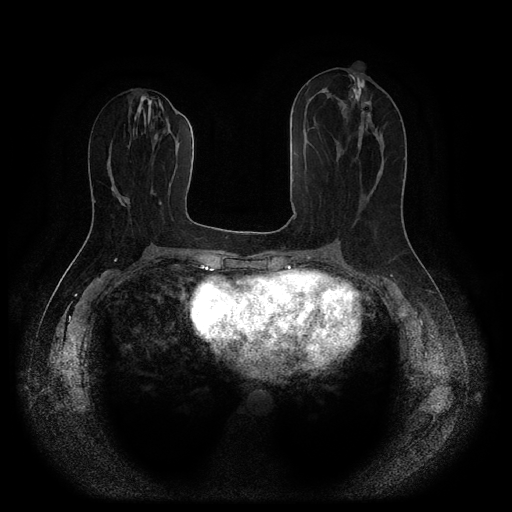
Breast MRI (dynamic contrast-enhanced, multi-phase), one axial slice. Slice 44 of 116 in the series (ordered by position). Dynamic contrast-enhanced series, time point 2 of 5 at this slice position (early post-contrast). 1.5 T. TE 2.6 ms, TR 5.3 ms. 512 × 512 image matrix, field of view 360 × 360 mm. Patient: female, 53 years.
Structures marked on this image (semi-automatic segmentation, software-assisted and operator-edited):
- breast lesion (labelled 'tumour' in the annotation; benign lesions carry a separate 'benign' label): bounding box [x1, y1, x2, y2] px = [361, 101, 371, 119]